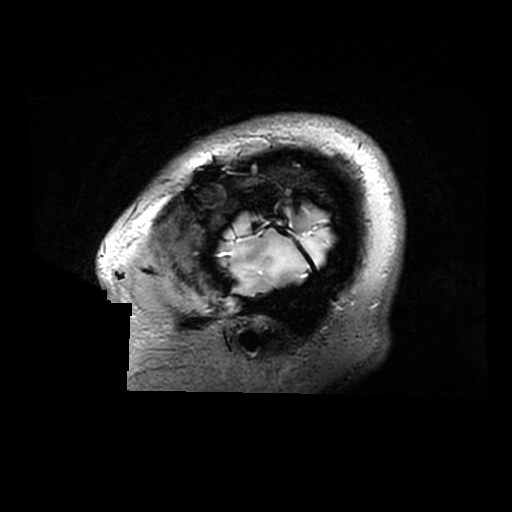
Brain MRI from a brain-tumour surgery series, one sagittal slice. 0.6 mm slice thickness. 512 × 512 image matrix. From the clinical record (not read from this slice): histopathology: Astrocytoma; WHO grade: 2; IDH mutation: yes.
Structures marked on this image (manually delineated by an expert):
- tumour: bounding box (x1, y1, x2, y2) in pixels: (221, 217, 333, 283)